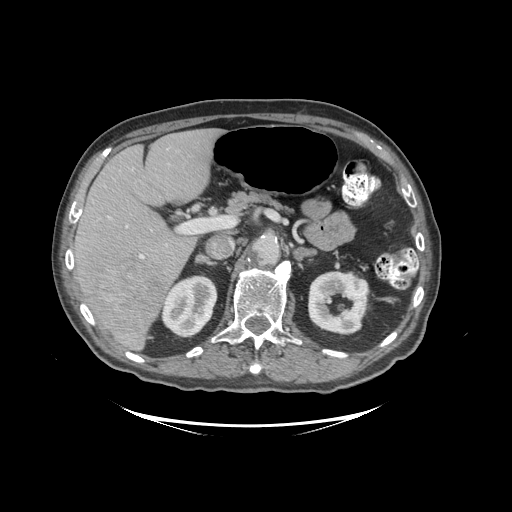
Contrast-enhanced abdominal CT (liver protocol), one axial slice; position 57 of 99 along the scan axis; reconstruction kernel STANDARD; soft-tissue window (W 400 / L 40 HU); 512 × 512 image matrix, field of view 460 × 460 mm. From the clinical record (not read from this slice): diagnosis: hepatocellular carcinoma (patient treated with transarterial chemoembolisation; whether this scan precedes or follows treatment is not stated here); TNM stage (as recorded): Stage-I; Child-Pugh class: A; tumour nodularity: uninodular.
Annotated regions visible in this slice (semi-automatically segmented with operator editing):
- liver parenchyma outside the tumour (the mass and vessels are separate outlines, so this box may not span the whole liver): bounding box <72,128,220,348> (left, top, right, bottom; pixels)
- mass: <79,252,169,342>
- liver vessels: <139,227,190,259>